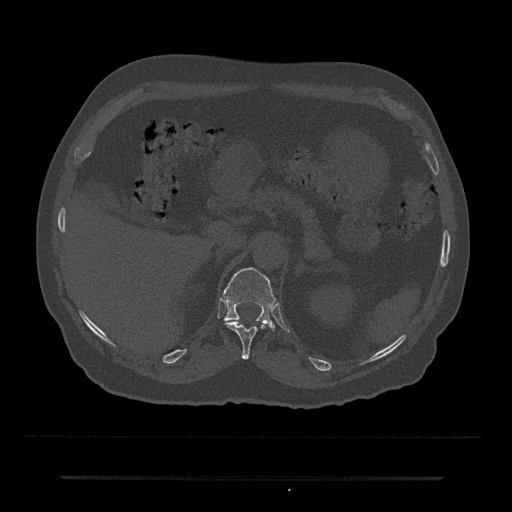
CT including the spine, one axial slice; position 151 of 797 along the scan axis; bone window (W 1800 / L 400 HU); 0.5 mm slice thickness; 512 × 512 image matrix, field of view 437 × 437 mm. Patient: male, 69 years. Case-level facts recorded for this patient, not image findings: primary cancer: prostate.
Annotated regions visible in this slice (semi-automatically segmented with operator editing):
- T11 vertebra: bounding box (x1, y1, x2, y2) in pixels: (225, 321, 265, 360)
- T12 vertebra: (223, 267, 276, 329)